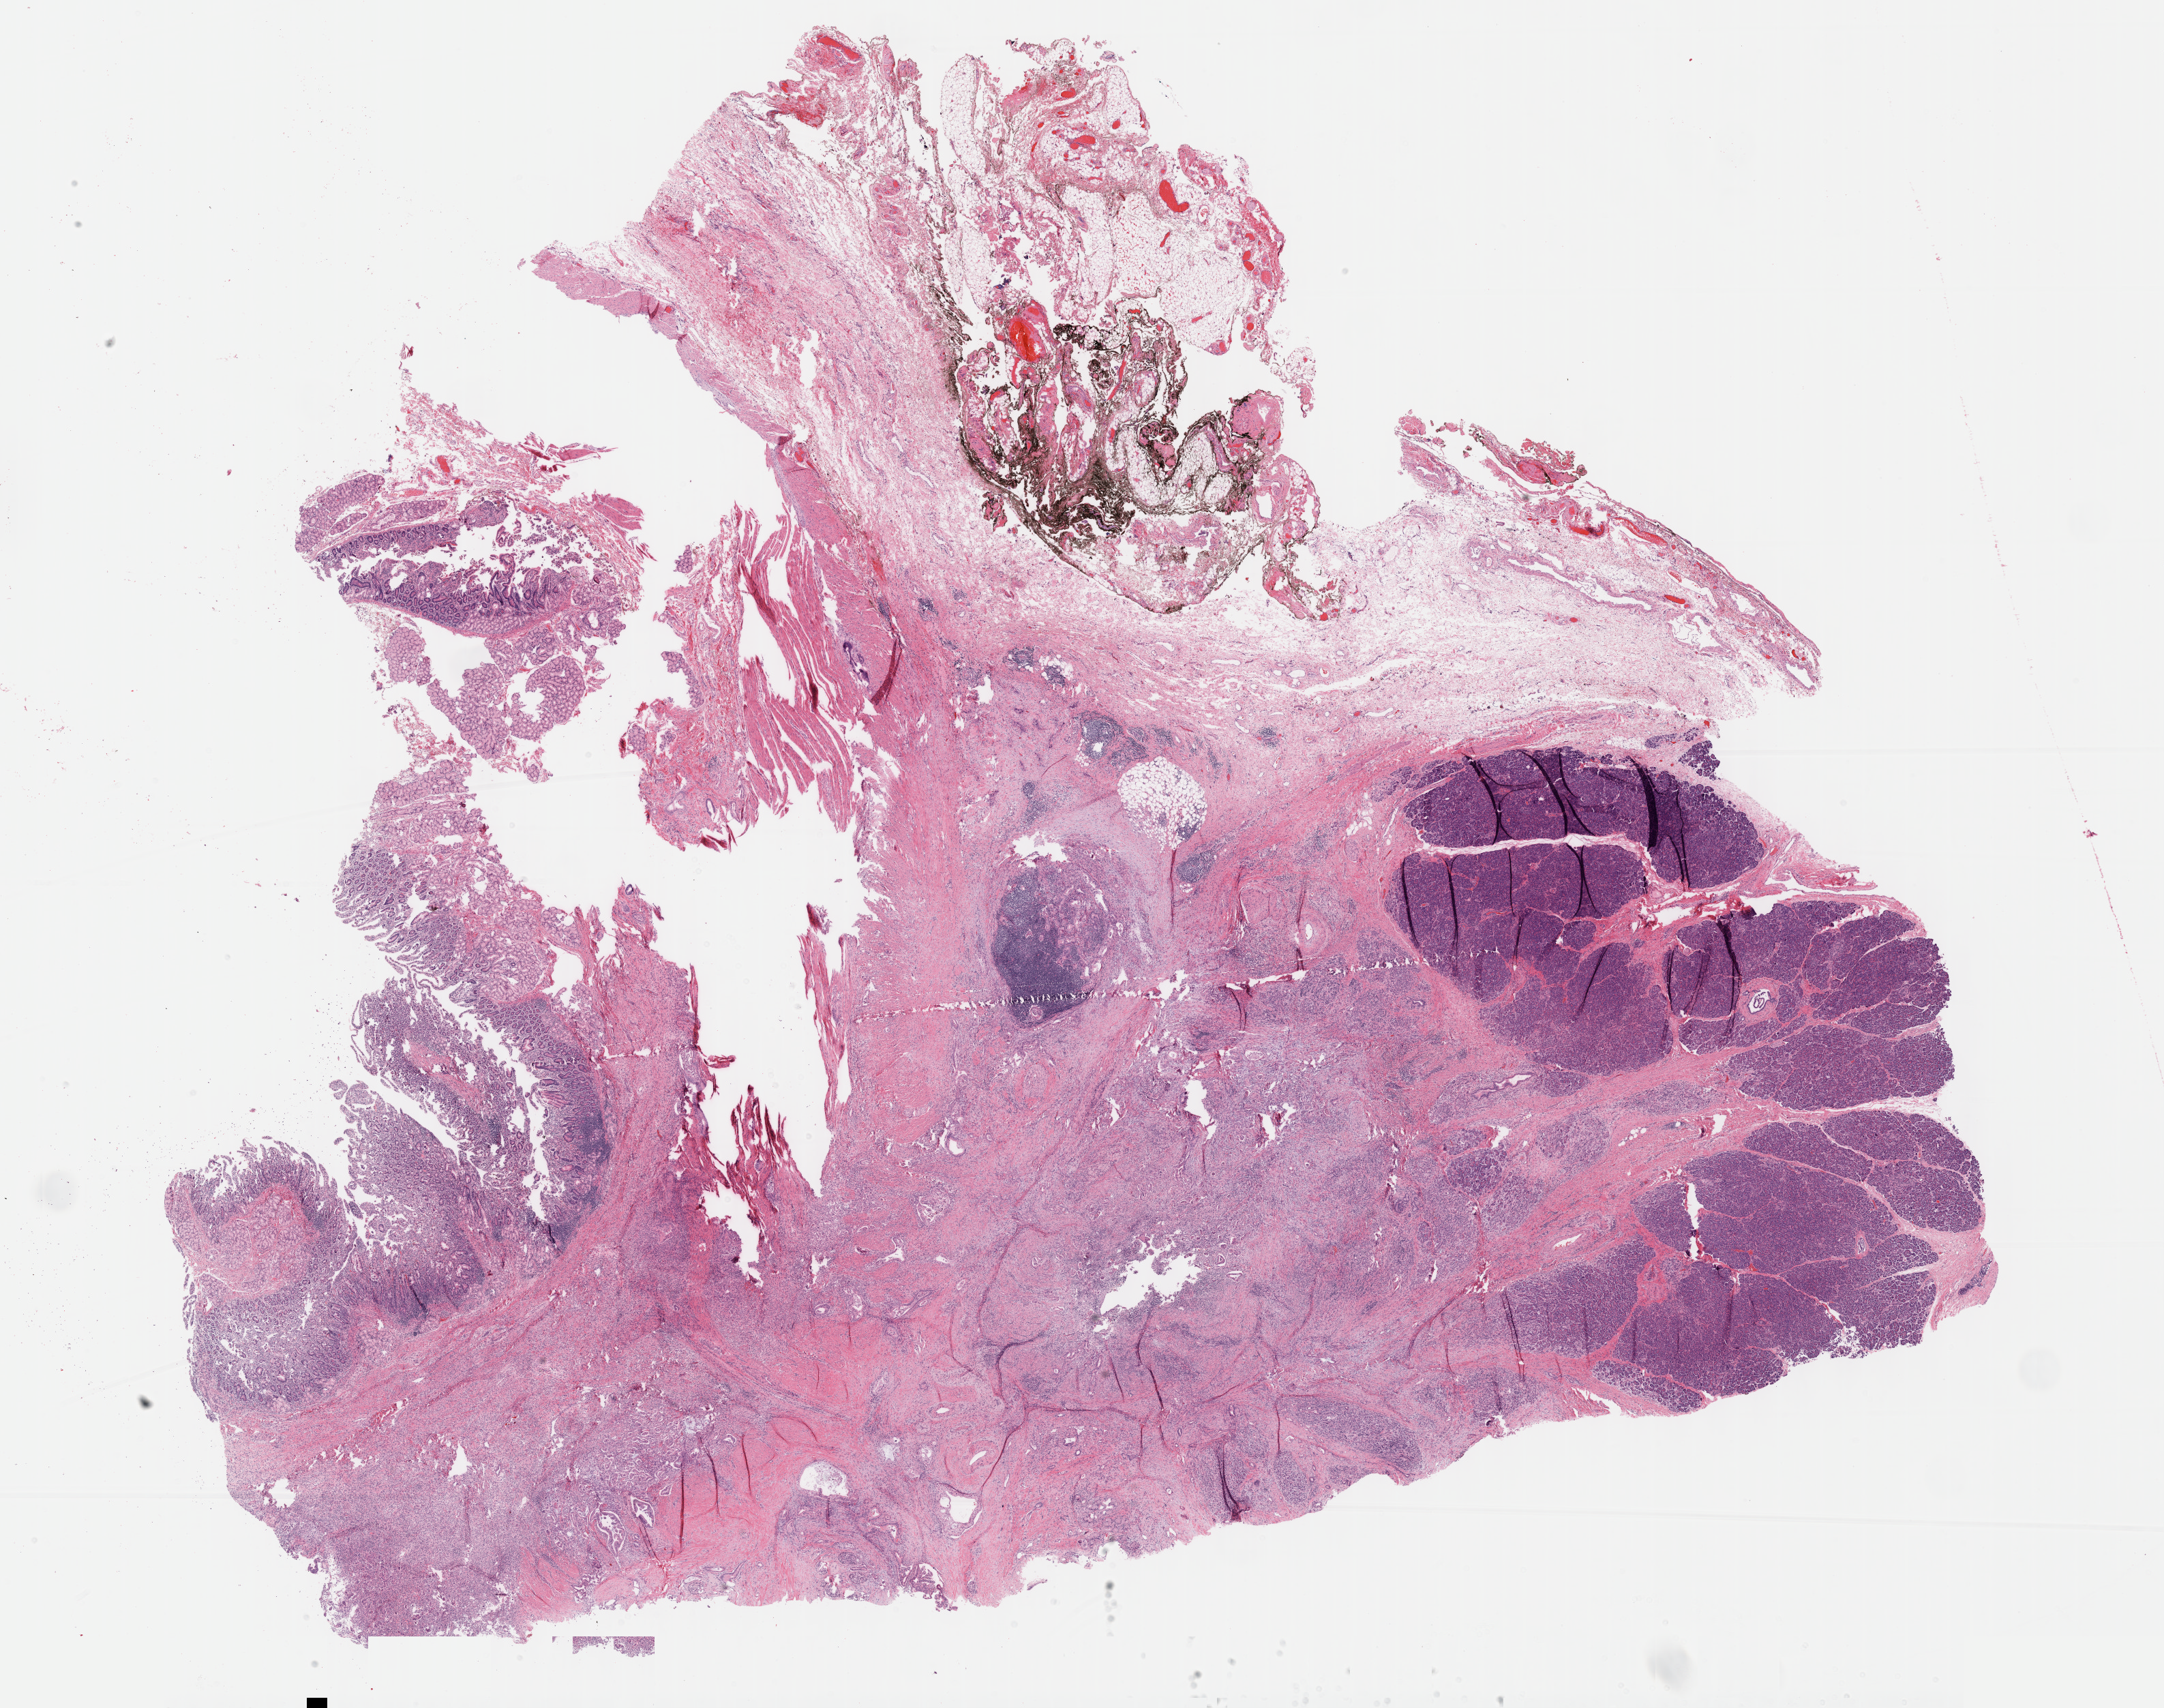
Digitized H&E-stained tissue section (whole slide) — a low-resolution overview of the entire scanned area, about 25.7 x 20.3 mm (from a 40x scan). Formalin-fixed paraffin-embedded (FFPE) diagnostic section. Primary tumour sample from the pancreas. Female, age 57 years at initial diagnosis. Histologic grade: G2 (moderately differentiated).
Diagnosis: Infiltrating duct carcinoma, NOS (head of pancreas). AJCC pathologic stage: IIB (7th edition). TNM: T3 N1 M0. Lymph nodes positive (case pathology): 7 of 30 examined.